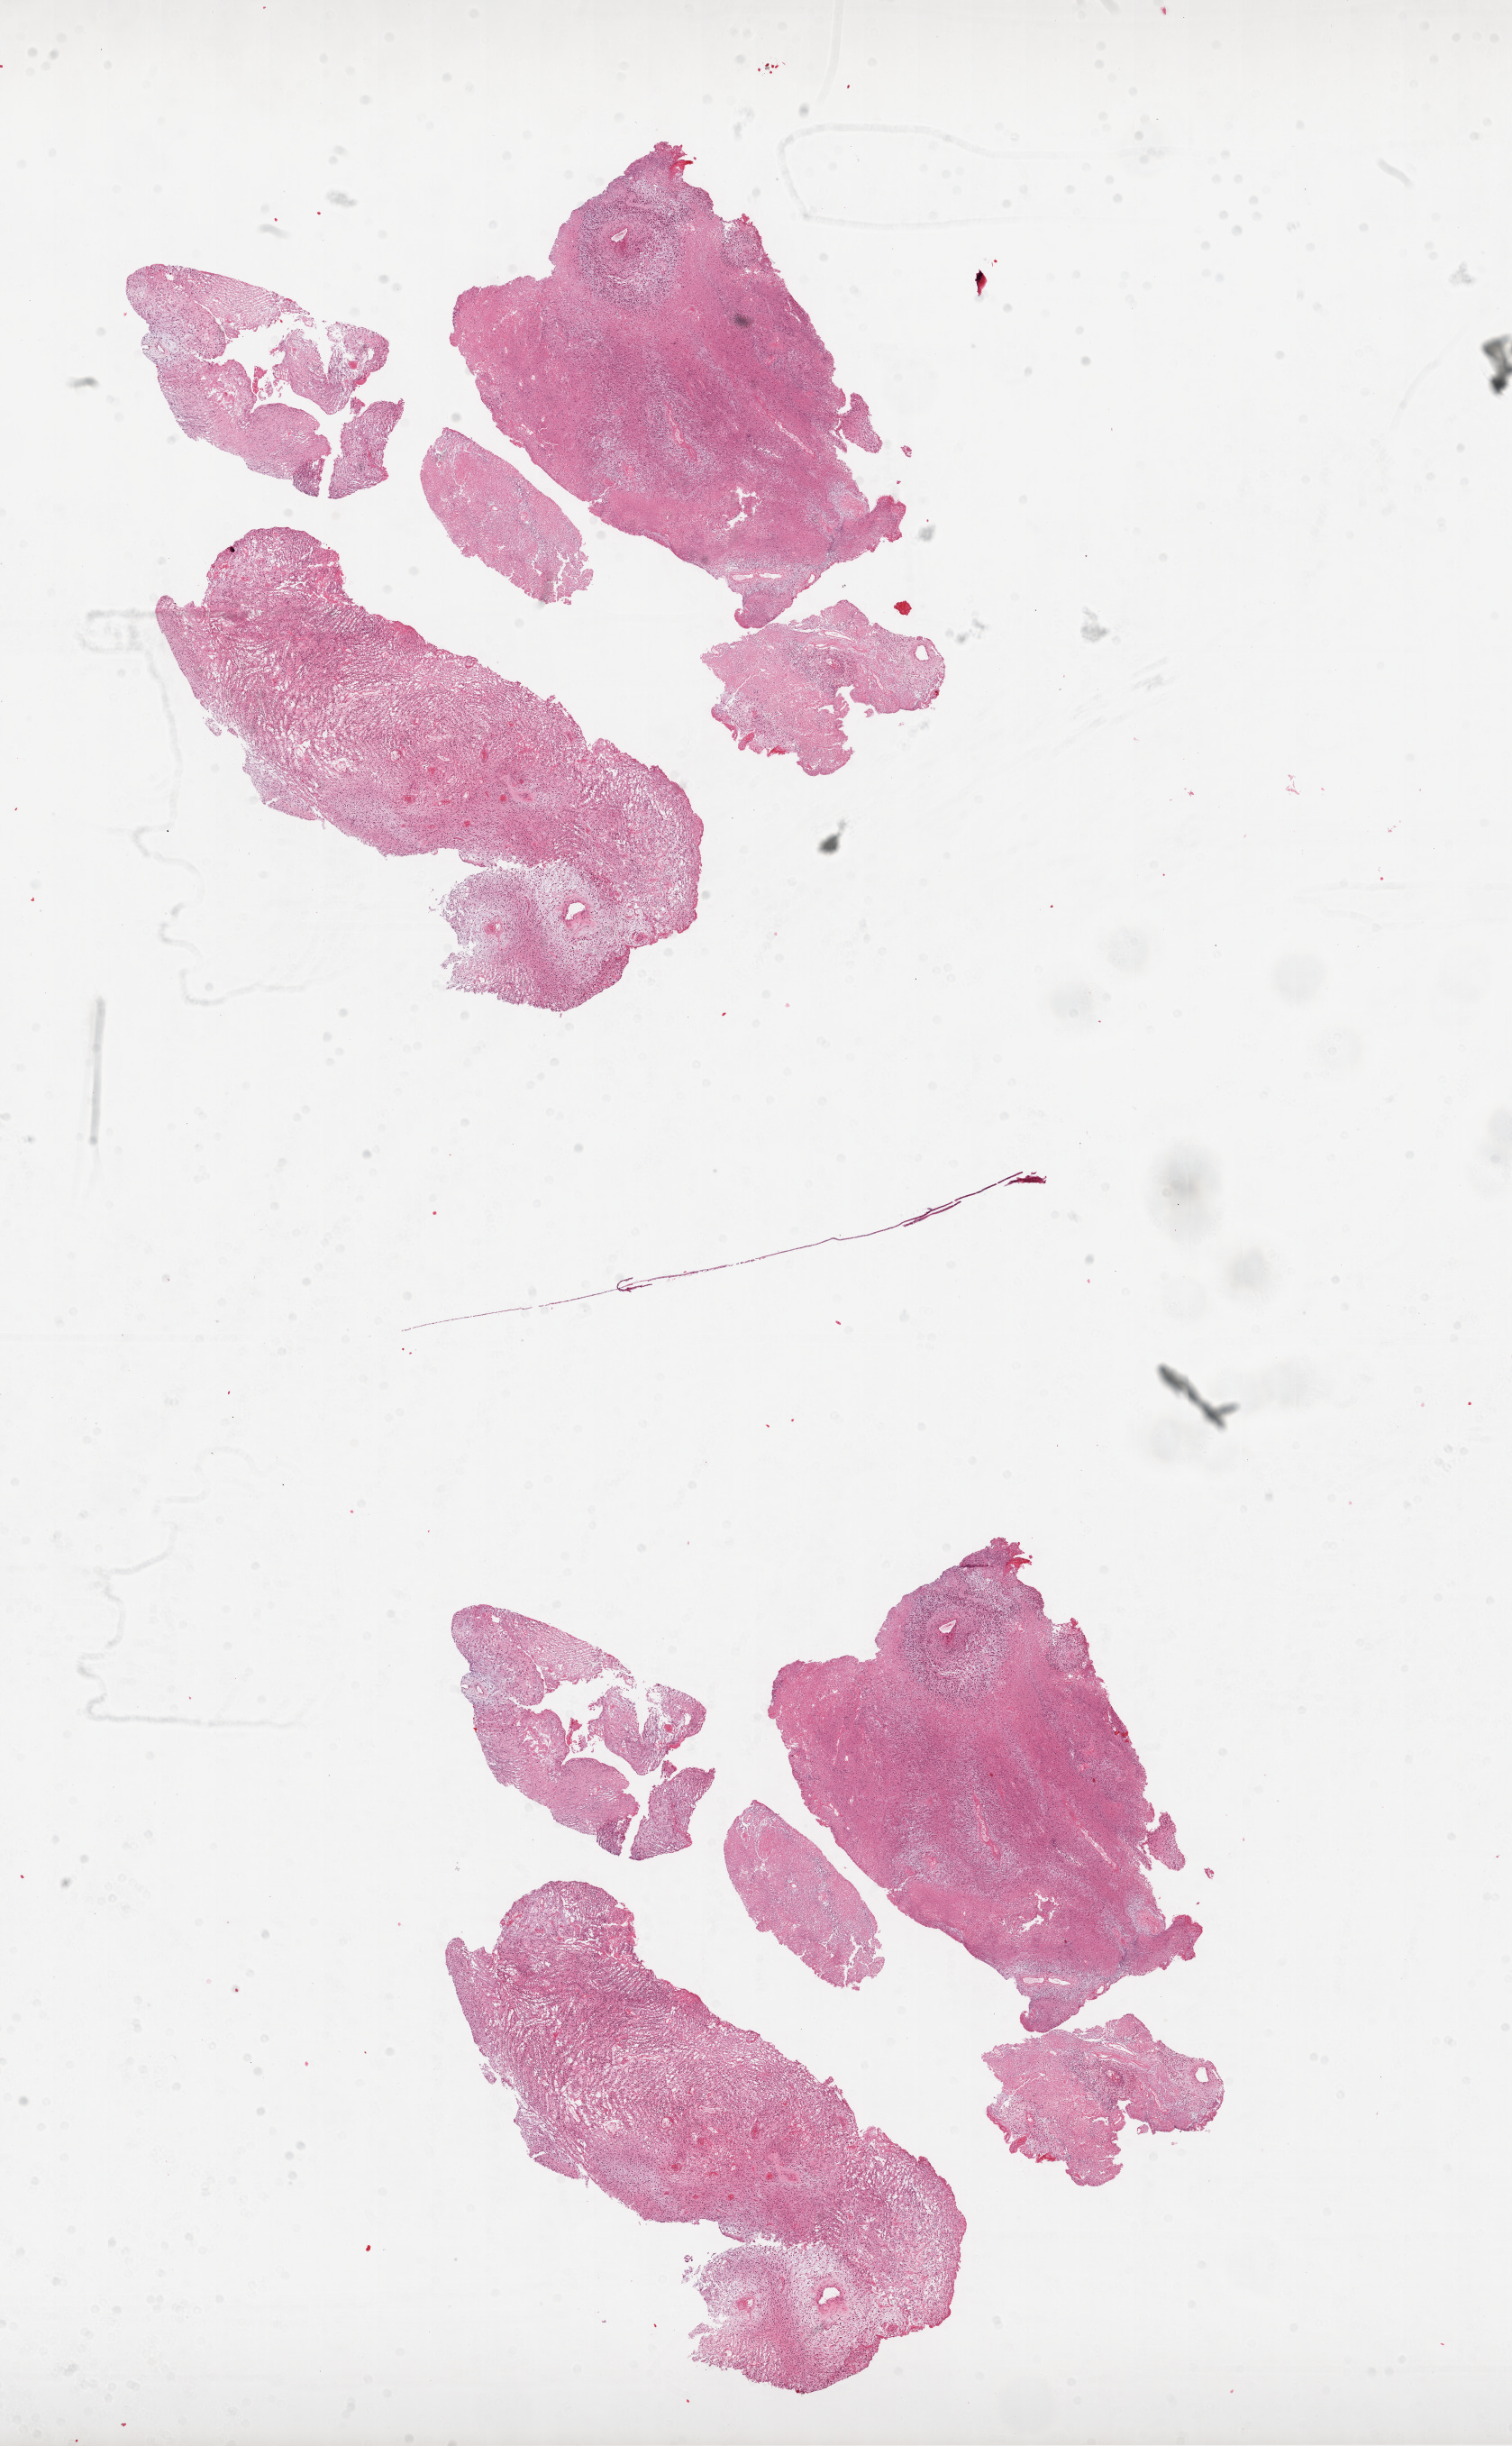
Whole-slide histology image, Hematoxylin and eosin (H&E) stained — a low-resolution overview of the entire scanned area, about 13.5 x 21.9 mm (from a 20x scan); formalin-fixed paraffin-embedded (FFPE) diagnostic section; sample: primary tumour, brain. Male, age 54 years at initial diagnosis.
* histologic diagnosis: Glioblastoma